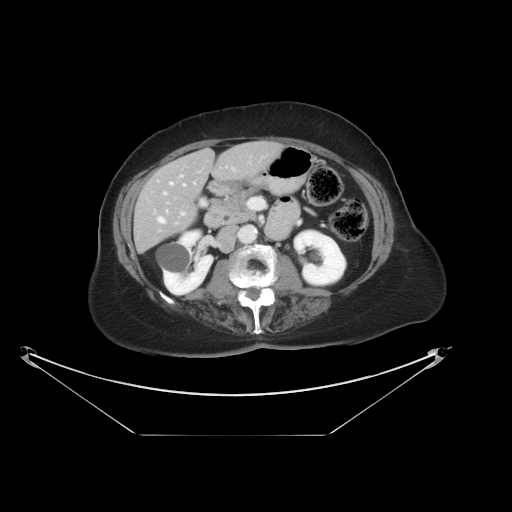
Contrast-enhanced abdominal CT, one axial slice. Slice 14 of 36 in the series (ordered by position). 120 kVp. Soft-tissue window (W 400 / L 40 HU). 512 × 512 image matrix. Female patient, age 70 years. Case-level facts recorded for this patient, not image findings: diagnosis: colorectal cancer liver metastases, imaged before liver resection; multiple liver metastases: no; largest metastasis: 2.5 cm; chemotherapy before resection: no.
Outlined on this slice (outlined manually by an expert reader):
- hepatic veins: bounding box [x1, y1, x2, y2] px = [158, 182, 186, 223]
- liver: [135, 142, 279, 250]
- planned liver remnant (the part of the liver to remain after resection): [135, 142, 280, 251]
- portal vein (with intrahepatic branches): [164, 192, 185, 215]